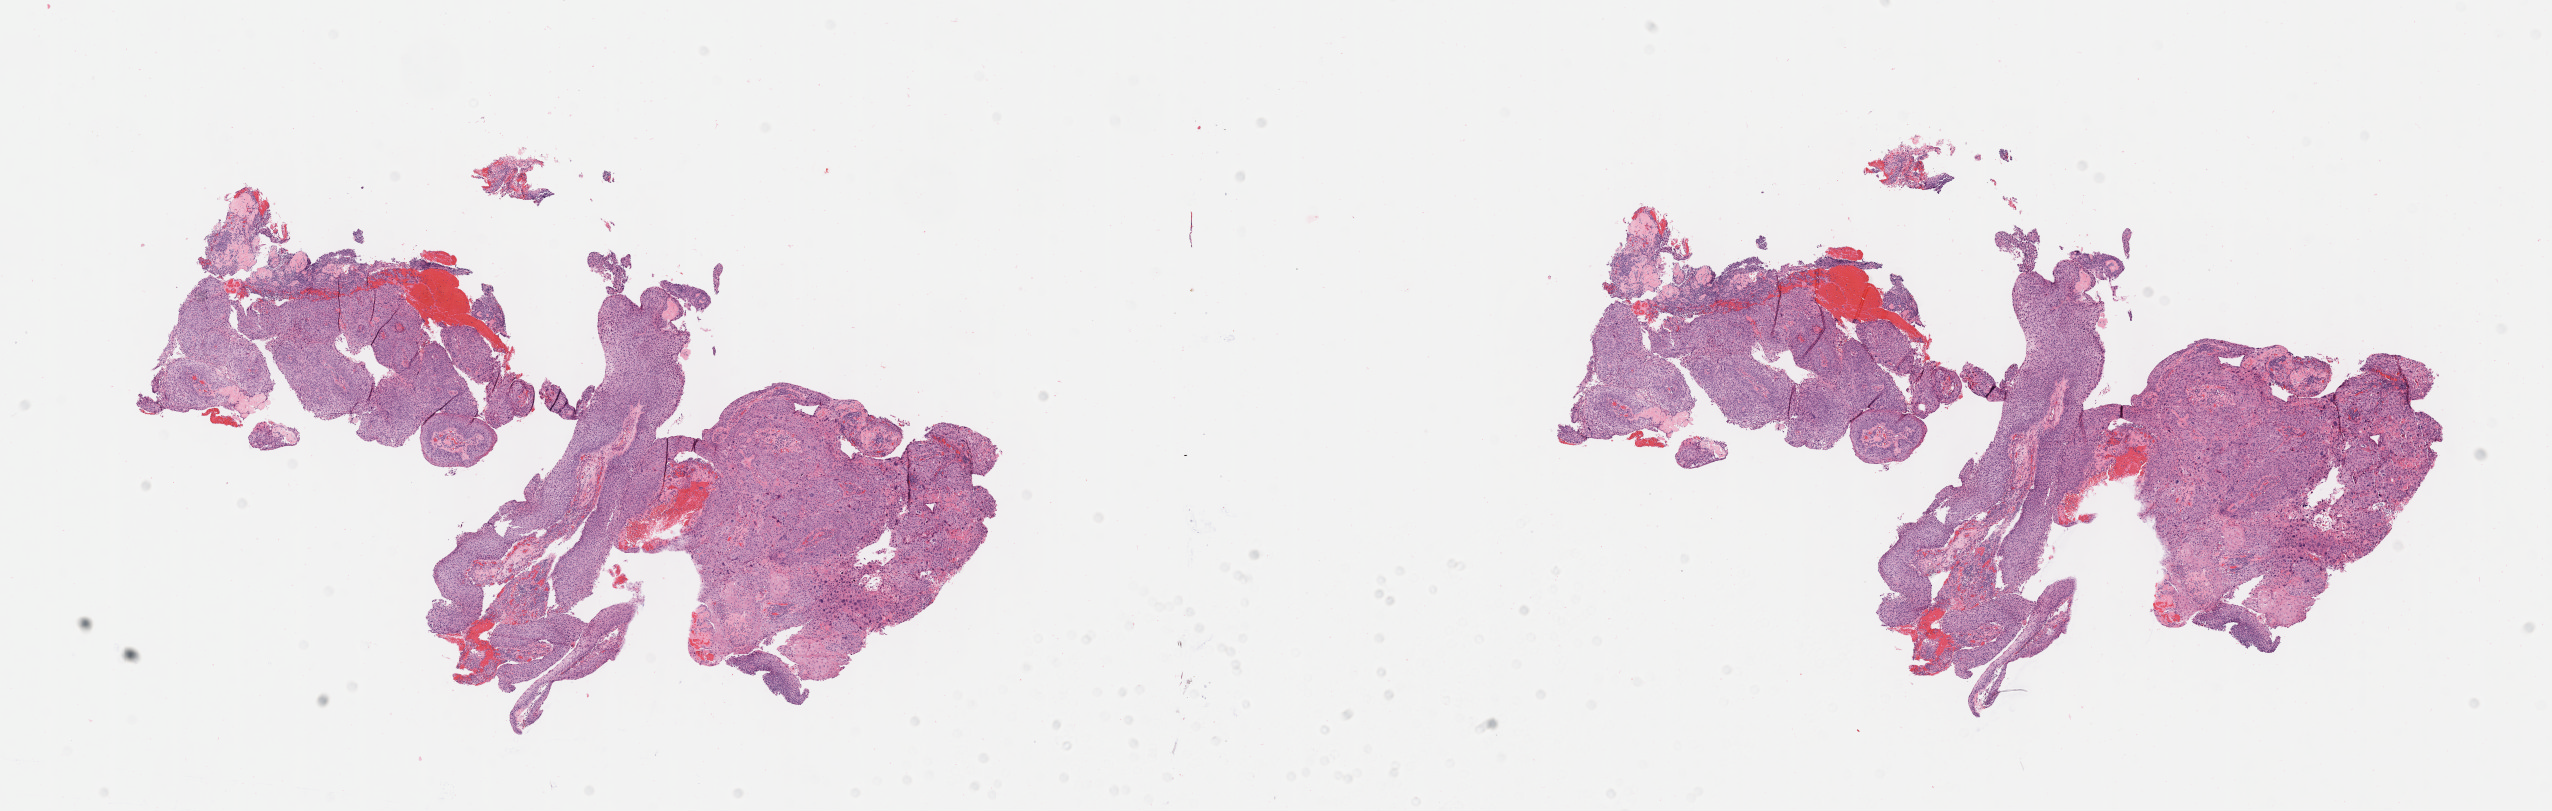
Digitized hematoxylin and eosin (H&E)-stained section — a low-resolution overview of the entire scanned area, about 20.6 x 6.6 mm. Tumor tissue. Site: cervix. Patient: female, 44 years old.
Diagnosis: Squamous cell carcinoma, keratinizing, NOS.